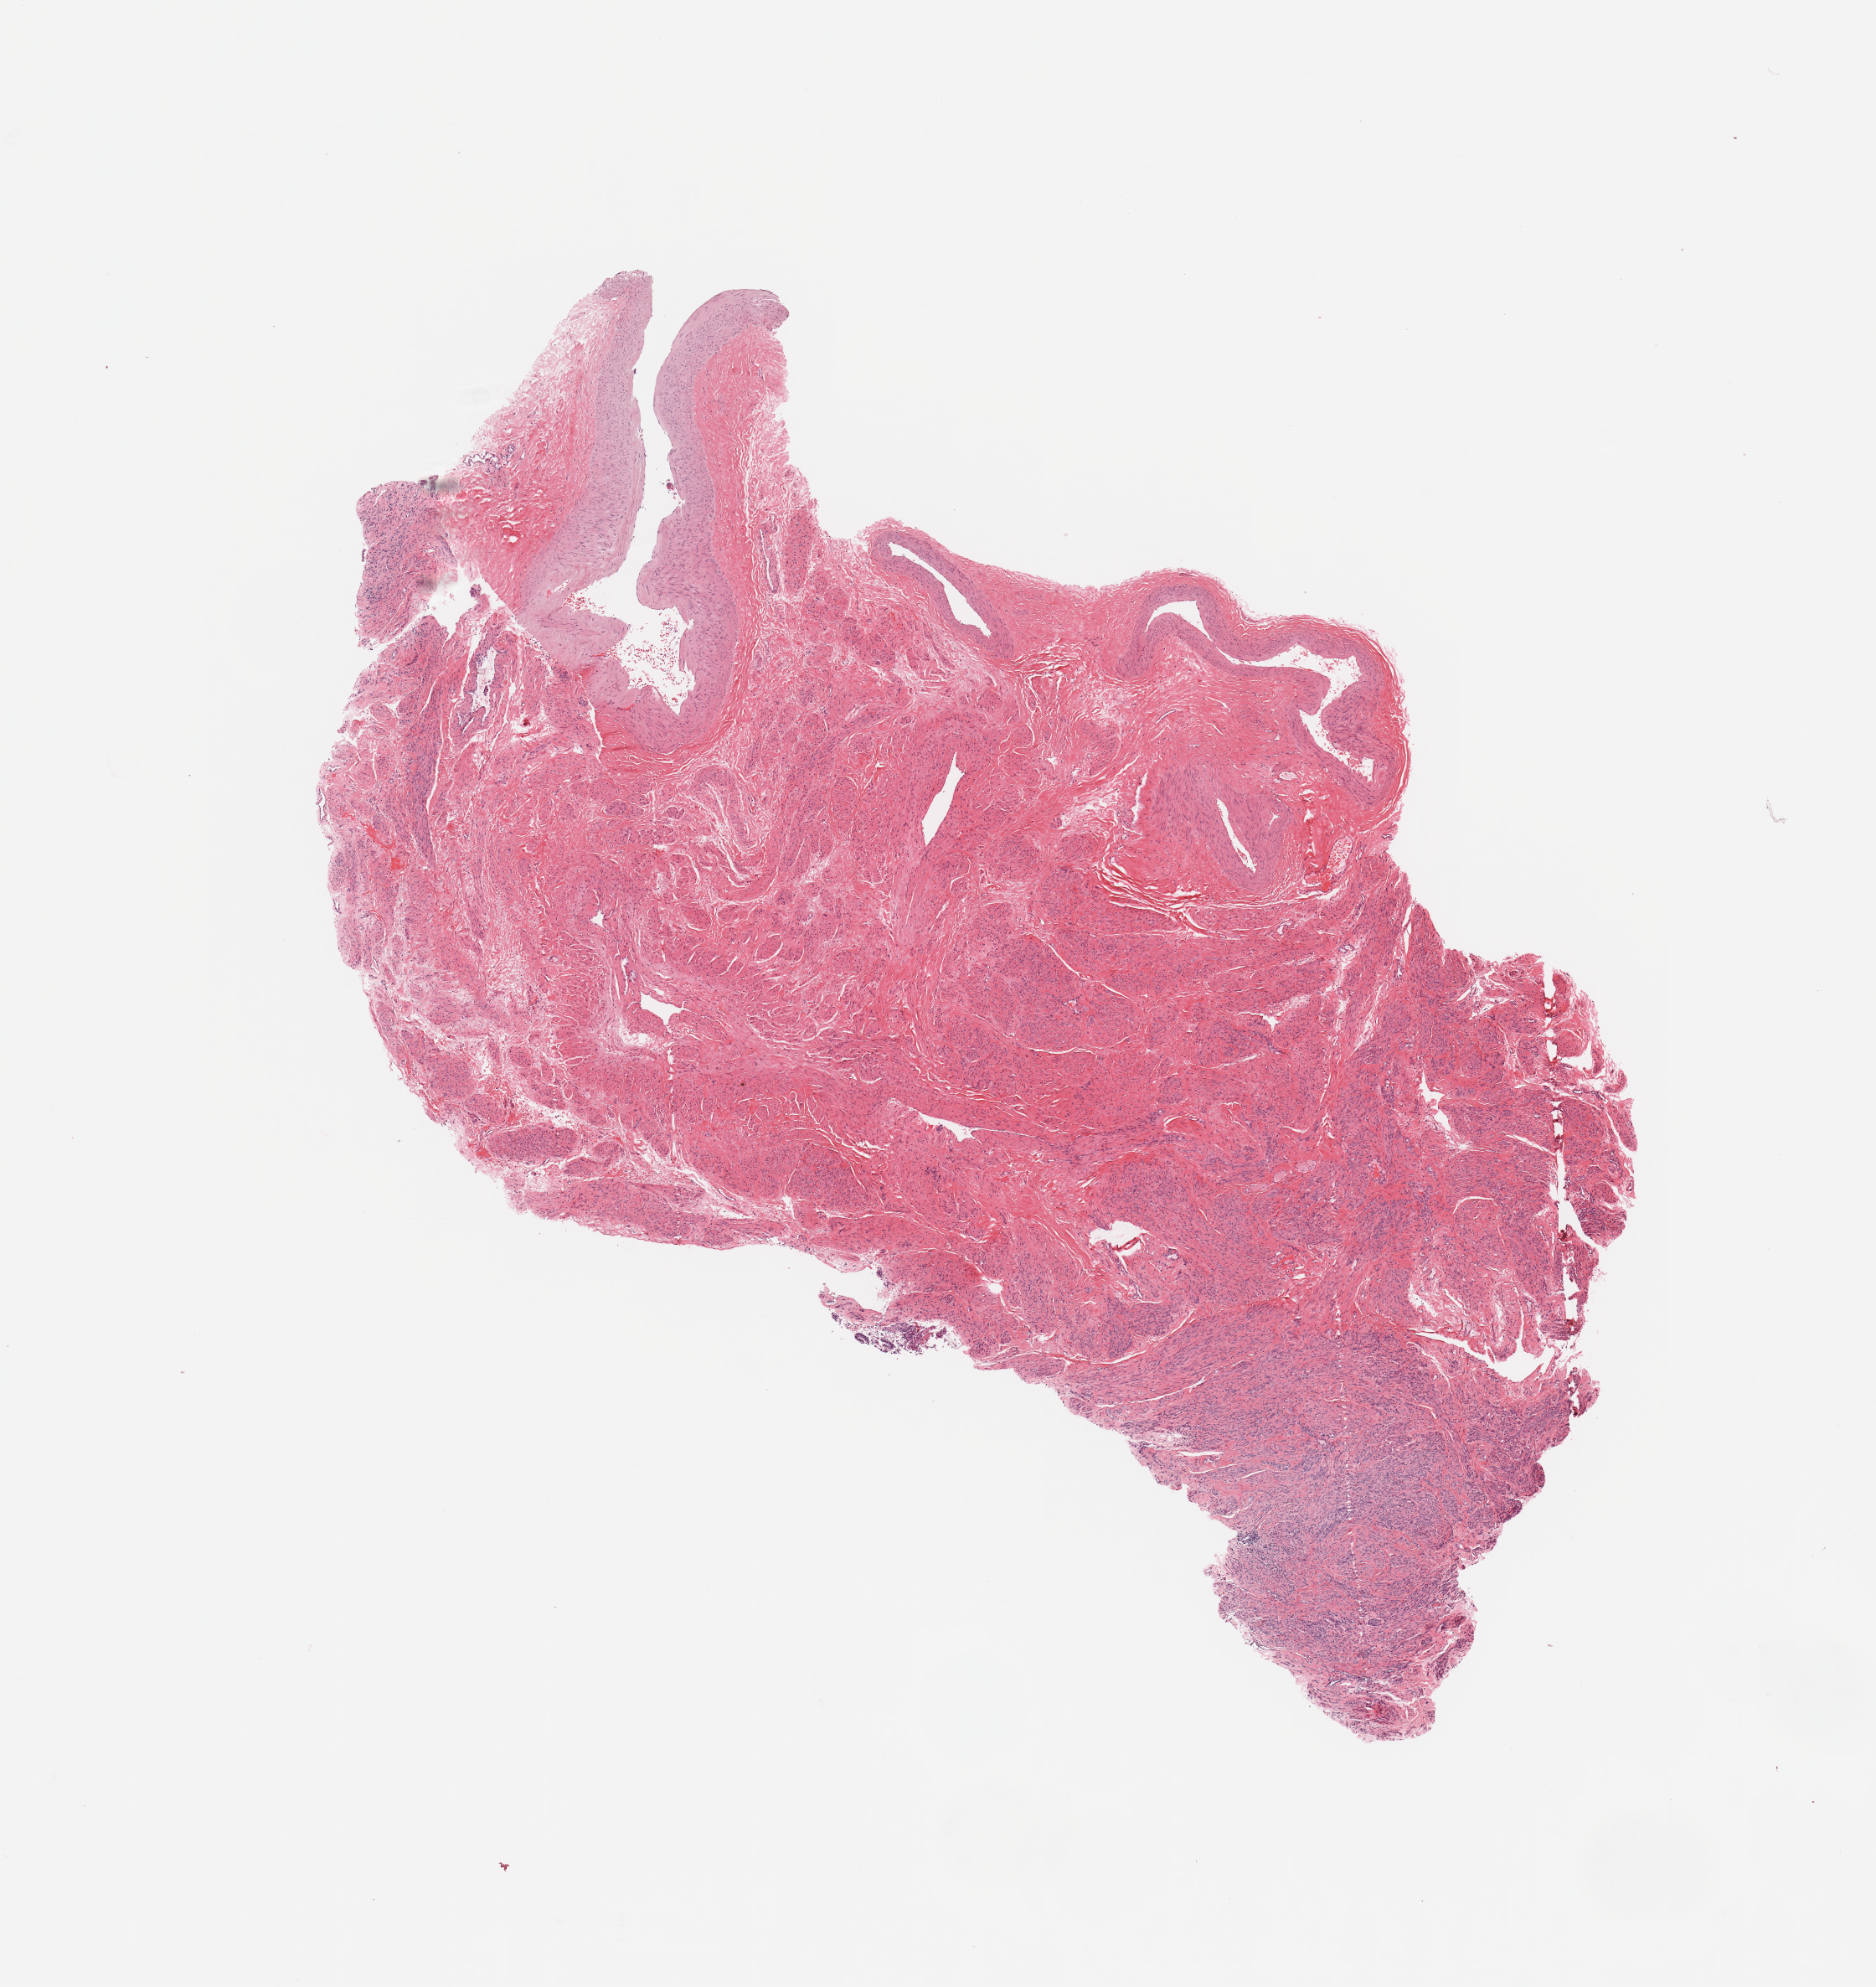
Digitized H&E tissue section (whole slide), a low-resolution overview of the entire scanned area, about 8.9 x 9.4 mm; normal (non-tumour) tissue sample, uterus. Patient: female, age 64 years.
This section: normal (non-tumour) tissue from the same patient. Patient diagnosis: Endometrioid adenocarcinoma, NOS.